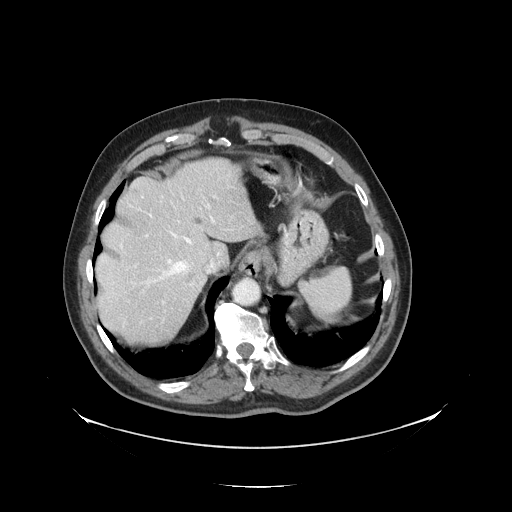
Contrast-enhanced abdominal CT, one axial slice; reconstruction kernel STANDARD; 120 kVp; intravenous contrast given; soft-tissue window (W 400 / L 40 HU); 2.5 mm slice thickness; 512 × 512 image matrix. Male patient, age 77 years. From the clinical record (not read from this slice): diagnosis: colorectal cancer liver metastases, imaged before liver resection; multiple liver metastases: no; largest metastasis: 1.5 cm; disease in both lobes: no.
Outlined on this slice (outlined manually by an expert reader):
- hepatic veins: bounding box <140,203,216,287> (left, top, right, bottom; pixels)
- liver: <97,160,256,346>
- planned liver remnant (the part of the liver to remain after resection): <97,160,257,290>
- portal vein (with intrahepatic branches): <134,188,233,319>
- liver metastasis: <196,218,203,225>